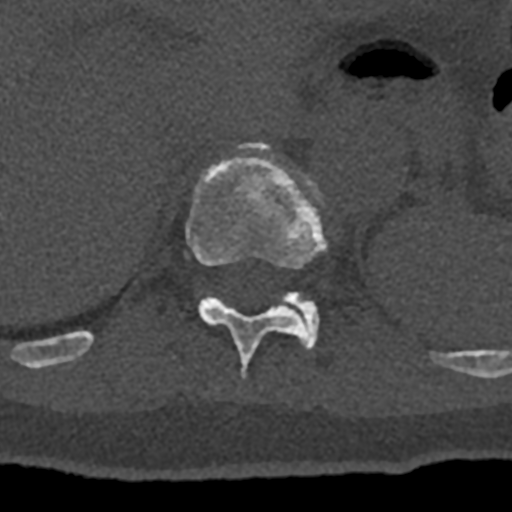
CT including the spine, one axial slice. Position 536 of 797 along the scan axis. Reconstruction kernel Br40s/3. Bone window (W 1800 / L 400 HU). 0.5 mm slice thickness. 512 × 512 image matrix, field of view 160 × 160 mm. Patient: male, 74 years. From the clinical record (not read from this slice): primary cancer: renal.
Outlined on this slice (semi-automatically segmented with operator editing):
- T11 vertebra: box from (x=70, y=142) to (x=327, y=380) px
- T12 vertebra: (x=281, y=291)–(x=319, y=349)